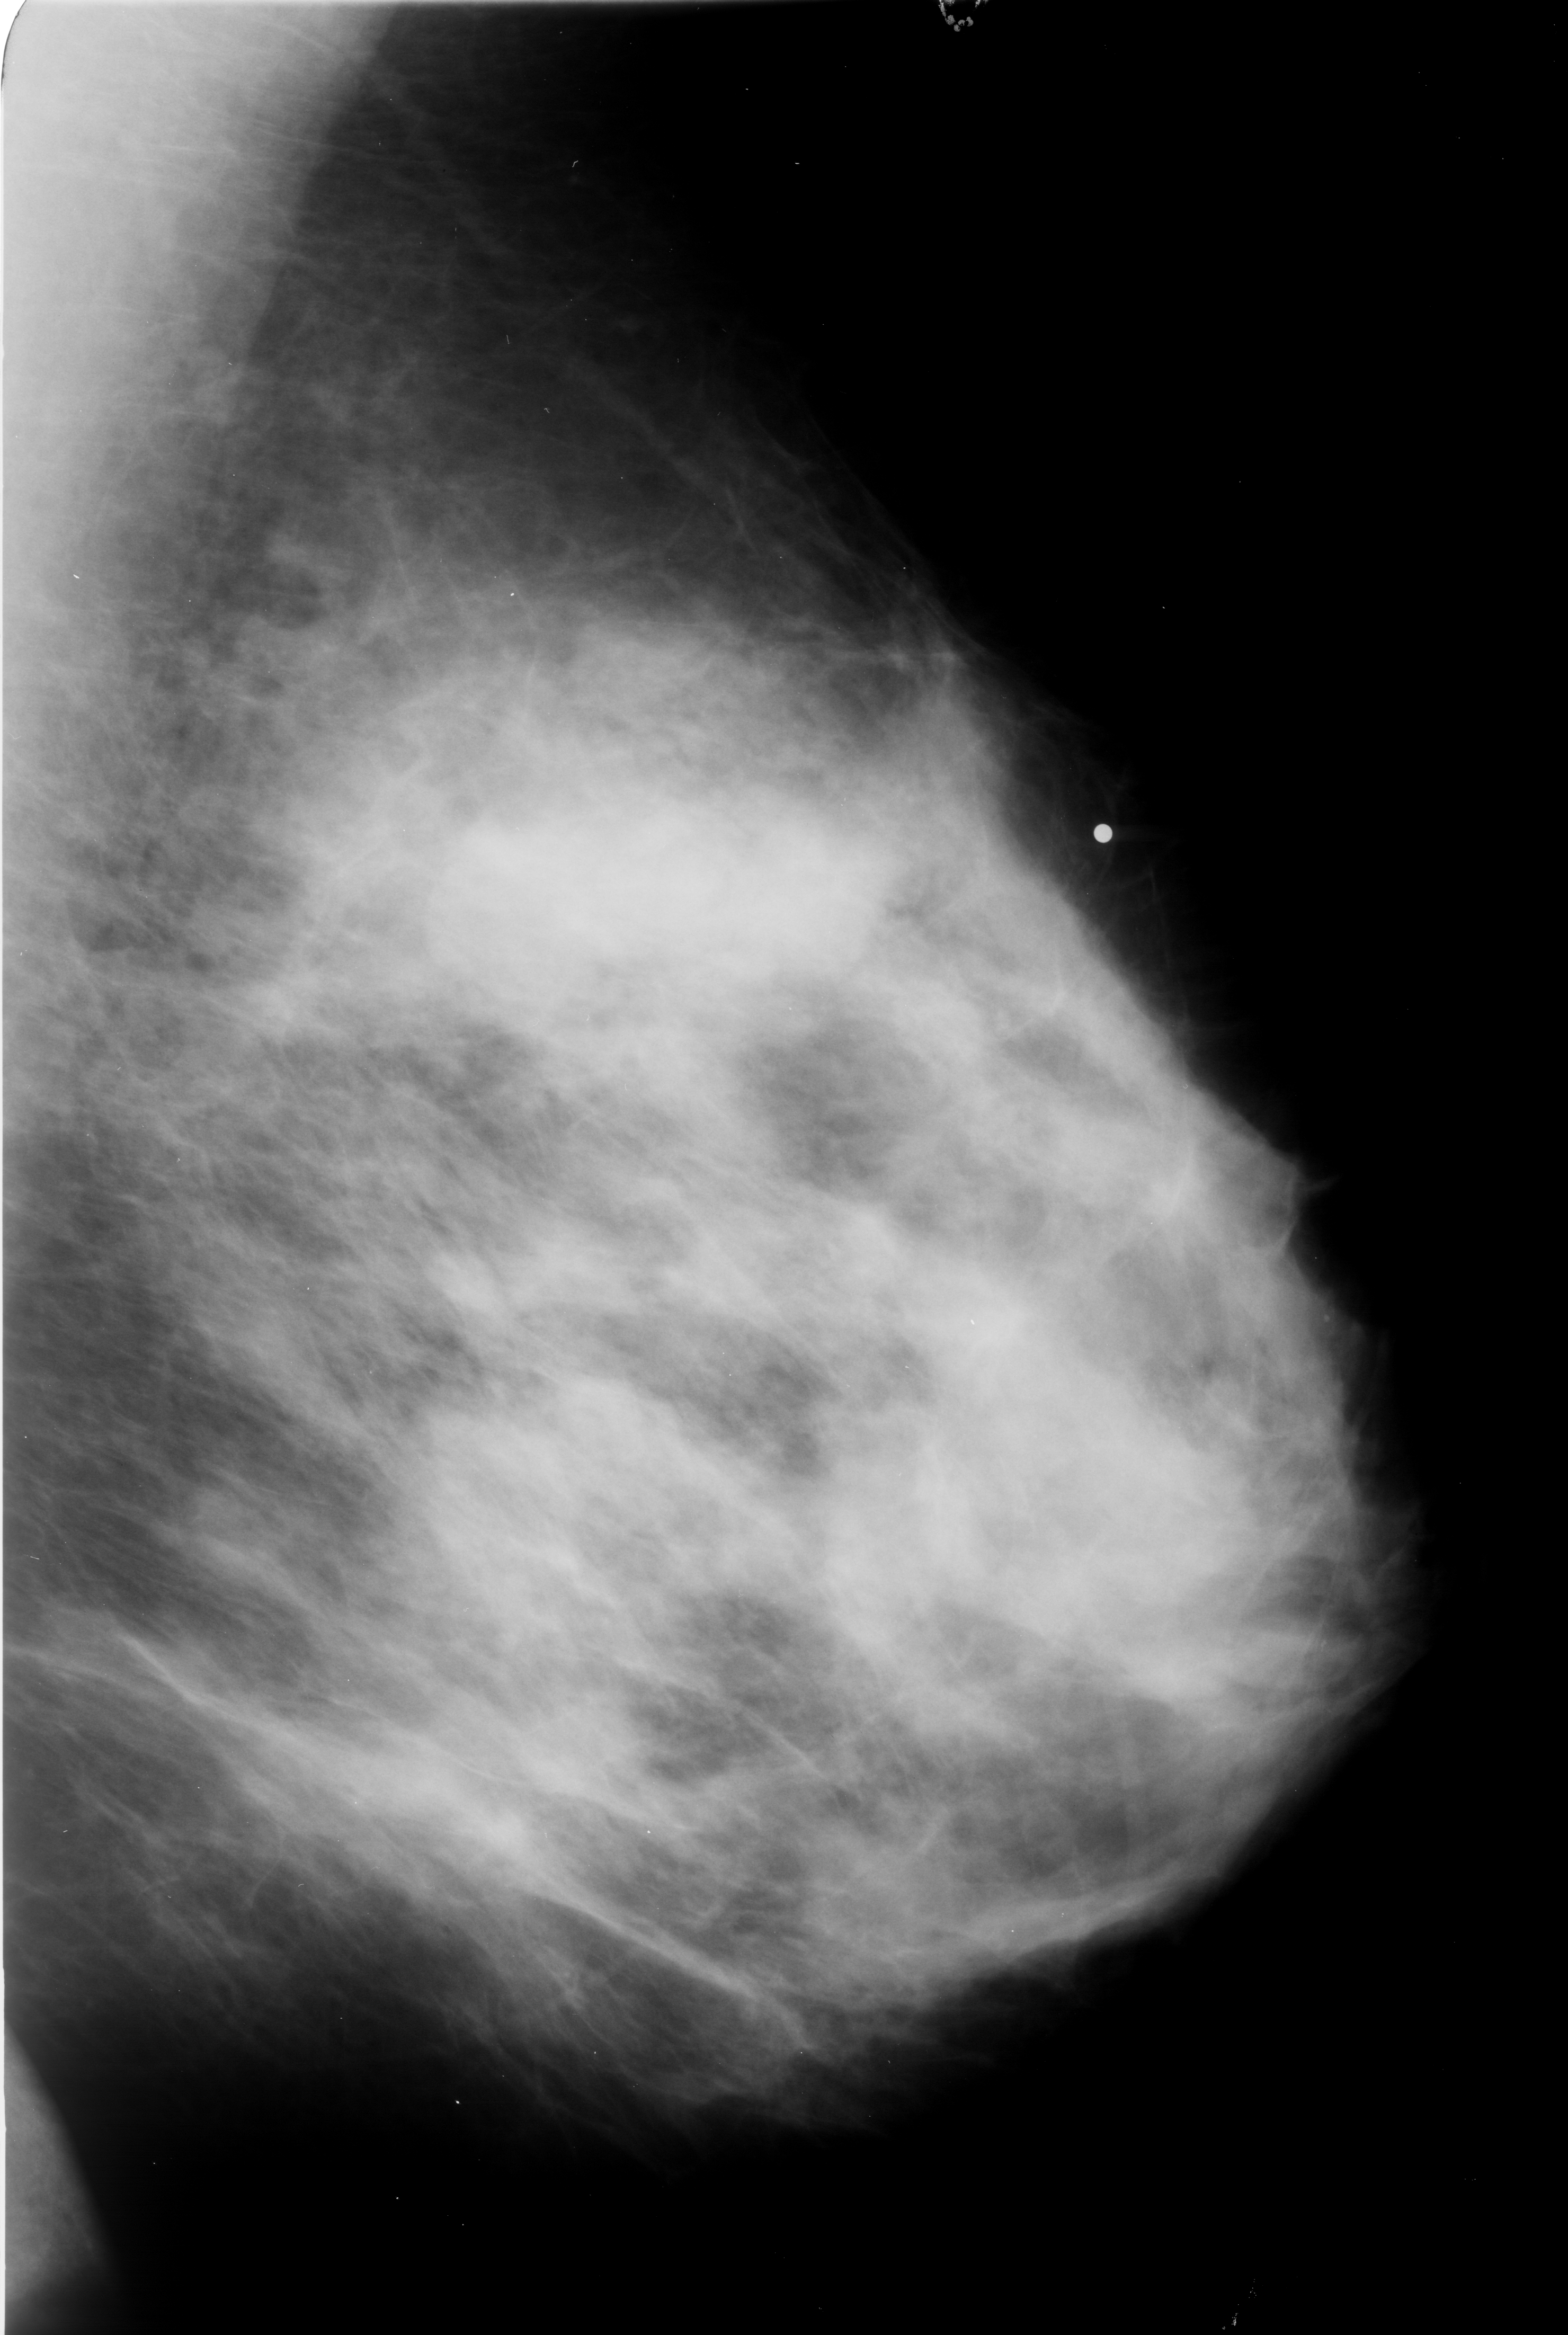
Scanned film-screen mammogram. Left breast. Mediolateral oblique (MLO) view. BI-RADS breast density category 3 (scale 1–4). 1568 × 2335 image matrix.
Expert-marked regions of interest on this film, with their recorded descriptors:
- mass, shape lobulated / irregular, margins obscured / ill defined; BI-RADS assessment category 4; pathology result (as recorded, not read from the image): malignant: box from (x=456, y=799) to (x=863, y=989) px